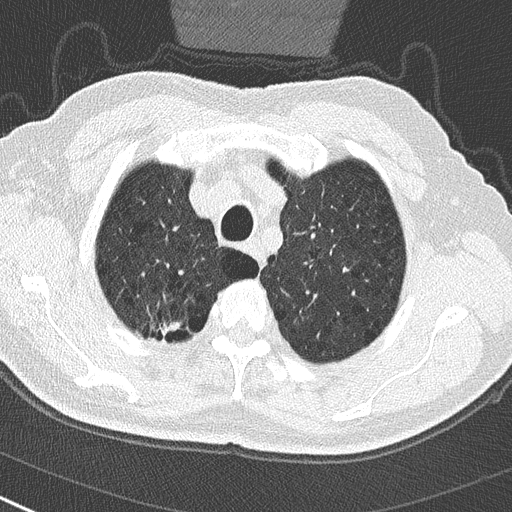
Low-dose screening chest CT, one axial slice; slice 243 of 290 in the series (ordered by position); 120 kVp; lung window (W 1500 / L -600 HU); 2 mm slice thickness; 512 × 512 image matrix, field of view 300 × 300 mm.
Annotated regions visible in this slice (expert manual segmentation):
- lesion 1 (tumor, upper lobe of right lung): bounding box [x1, y1, x2, y2] px = [152, 319, 182, 342]